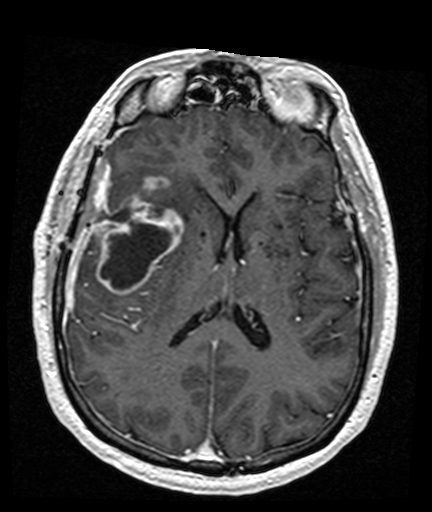
Brain MRI from a brain-tumour surgery series, one axial slice; position 74 of 176 along the scan axis; T1-weighted post-contrast; 432 × 512 image matrix, field of view 194 × 230 mm. Case-level facts recorded for this patient, not image findings: histopathology: Glioblastoma; WHO grade: 4; IDH mutation: no.
Annotated regions visible in this slice (outlined manually by an expert reader):
- tumour: bounding box [x1, y1, x2, y2] px = [95, 176, 184, 296]